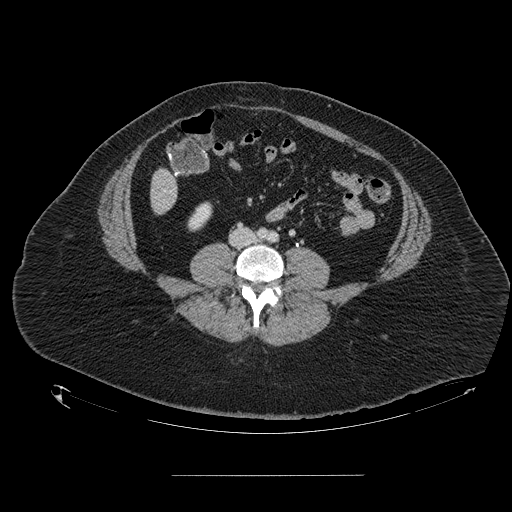
Contrast-enhanced abdominal CT, one axial slice. Slice 14 of 164 in the series (ordered by position). 120 kVp. Intravenous contrast given. Soft-tissue window (W 400 / L 40 HU). 512 × 512 image matrix, field of view 495 × 495 mm. Female patient, age 52 years. From the clinical record (not read from this slice): diagnosis: colorectal cancer liver metastases, imaged before liver resection; multiple liver metastases: yes; largest metastasis: 3.5 cm; disease in both lobes: no.
Structures marked on this image (manually delineated by an expert):
- liver: box from (x=151, y=170) to (x=177, y=213) px